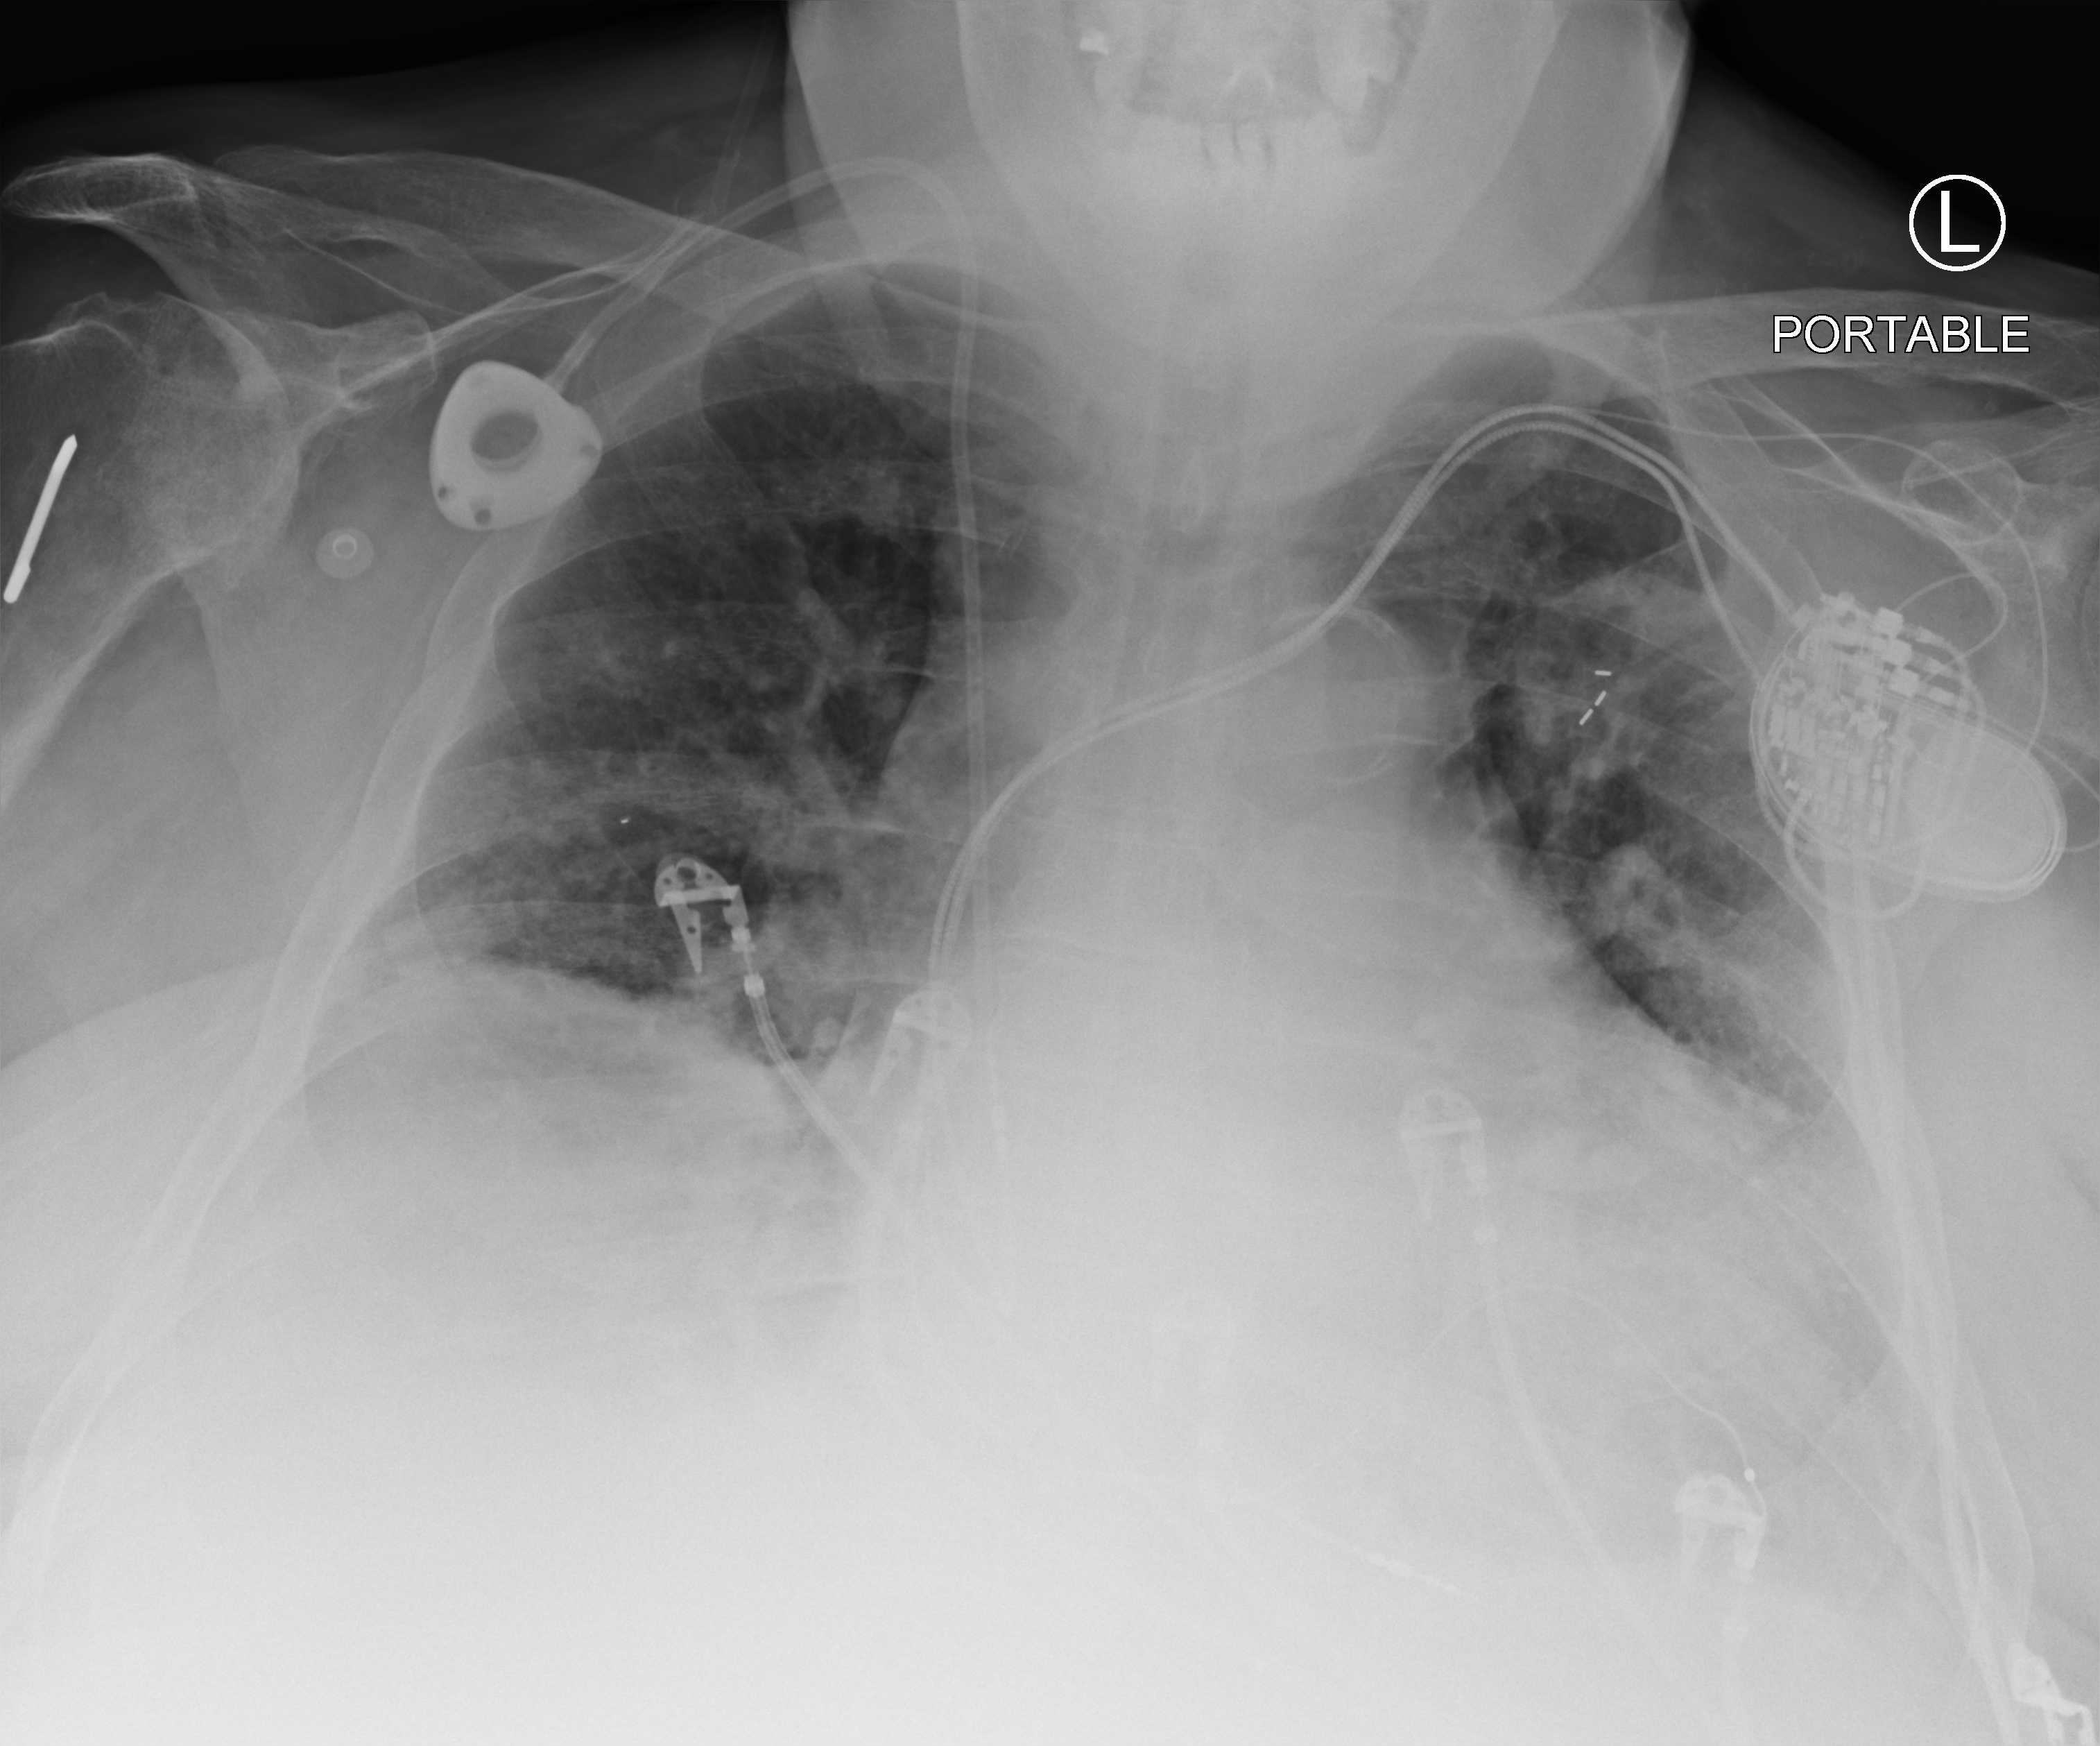
Portable chest radiograph; anteroposterior (AP) projection. Patient hospitalised with COVID-19; male, aged 60–74 years.
From the hospital-stay record, not from the radiograph (when in the stay this image was taken is not recorded): admitted to intensive care during this hospital stay: yes; mechanically ventilated during this hospital stay: no.